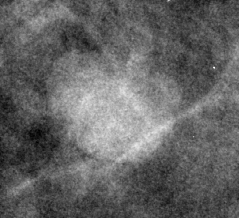
Cropped region of a digitized screen-film mammogram centred on a radiologist-marked abnormality; right breast; CC view.
- Finding: mass, shape lymph node; BI-RADS assessment category 2; benign; no additional work-up was recommended (benign without callback).